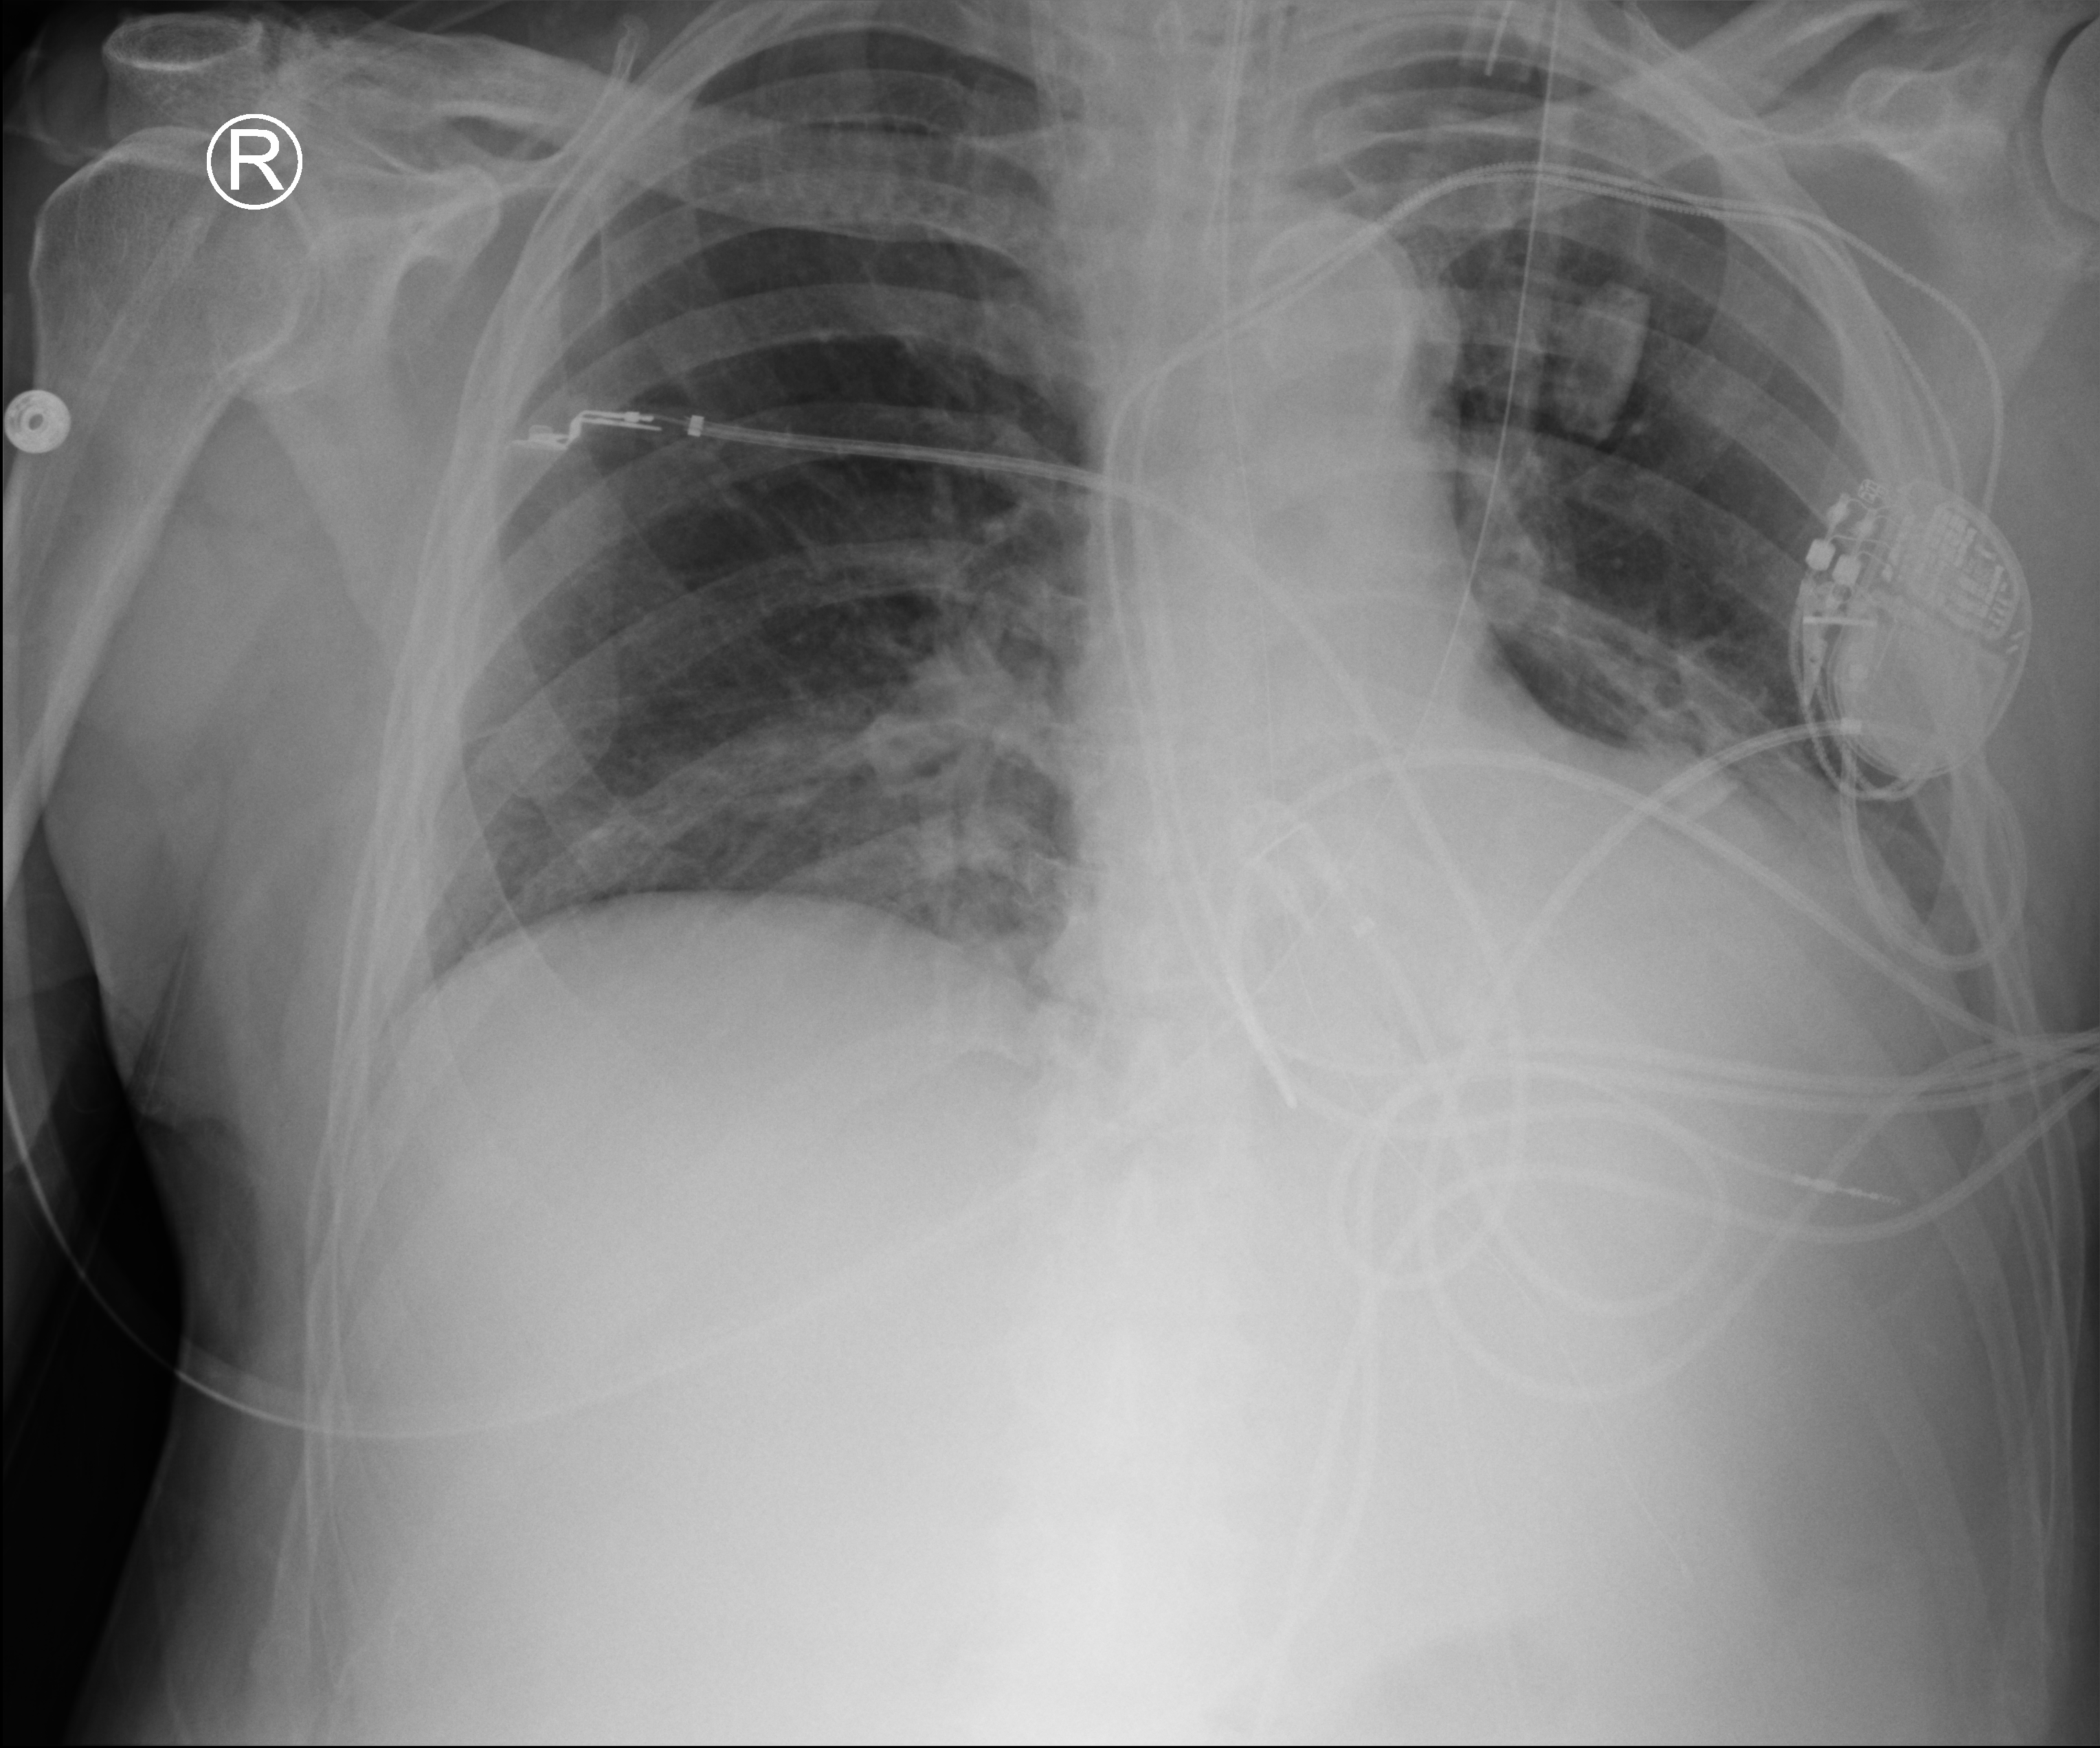
Bedside chest radiograph (computed radiography), anteroposterior (AP) projection. Male patient hospitalised with COVID-19, age 60–74 years.
Admission-level facts for this patient (not findings on this image; timing relative to this image not recorded):
- length of hospital stay: 41 days